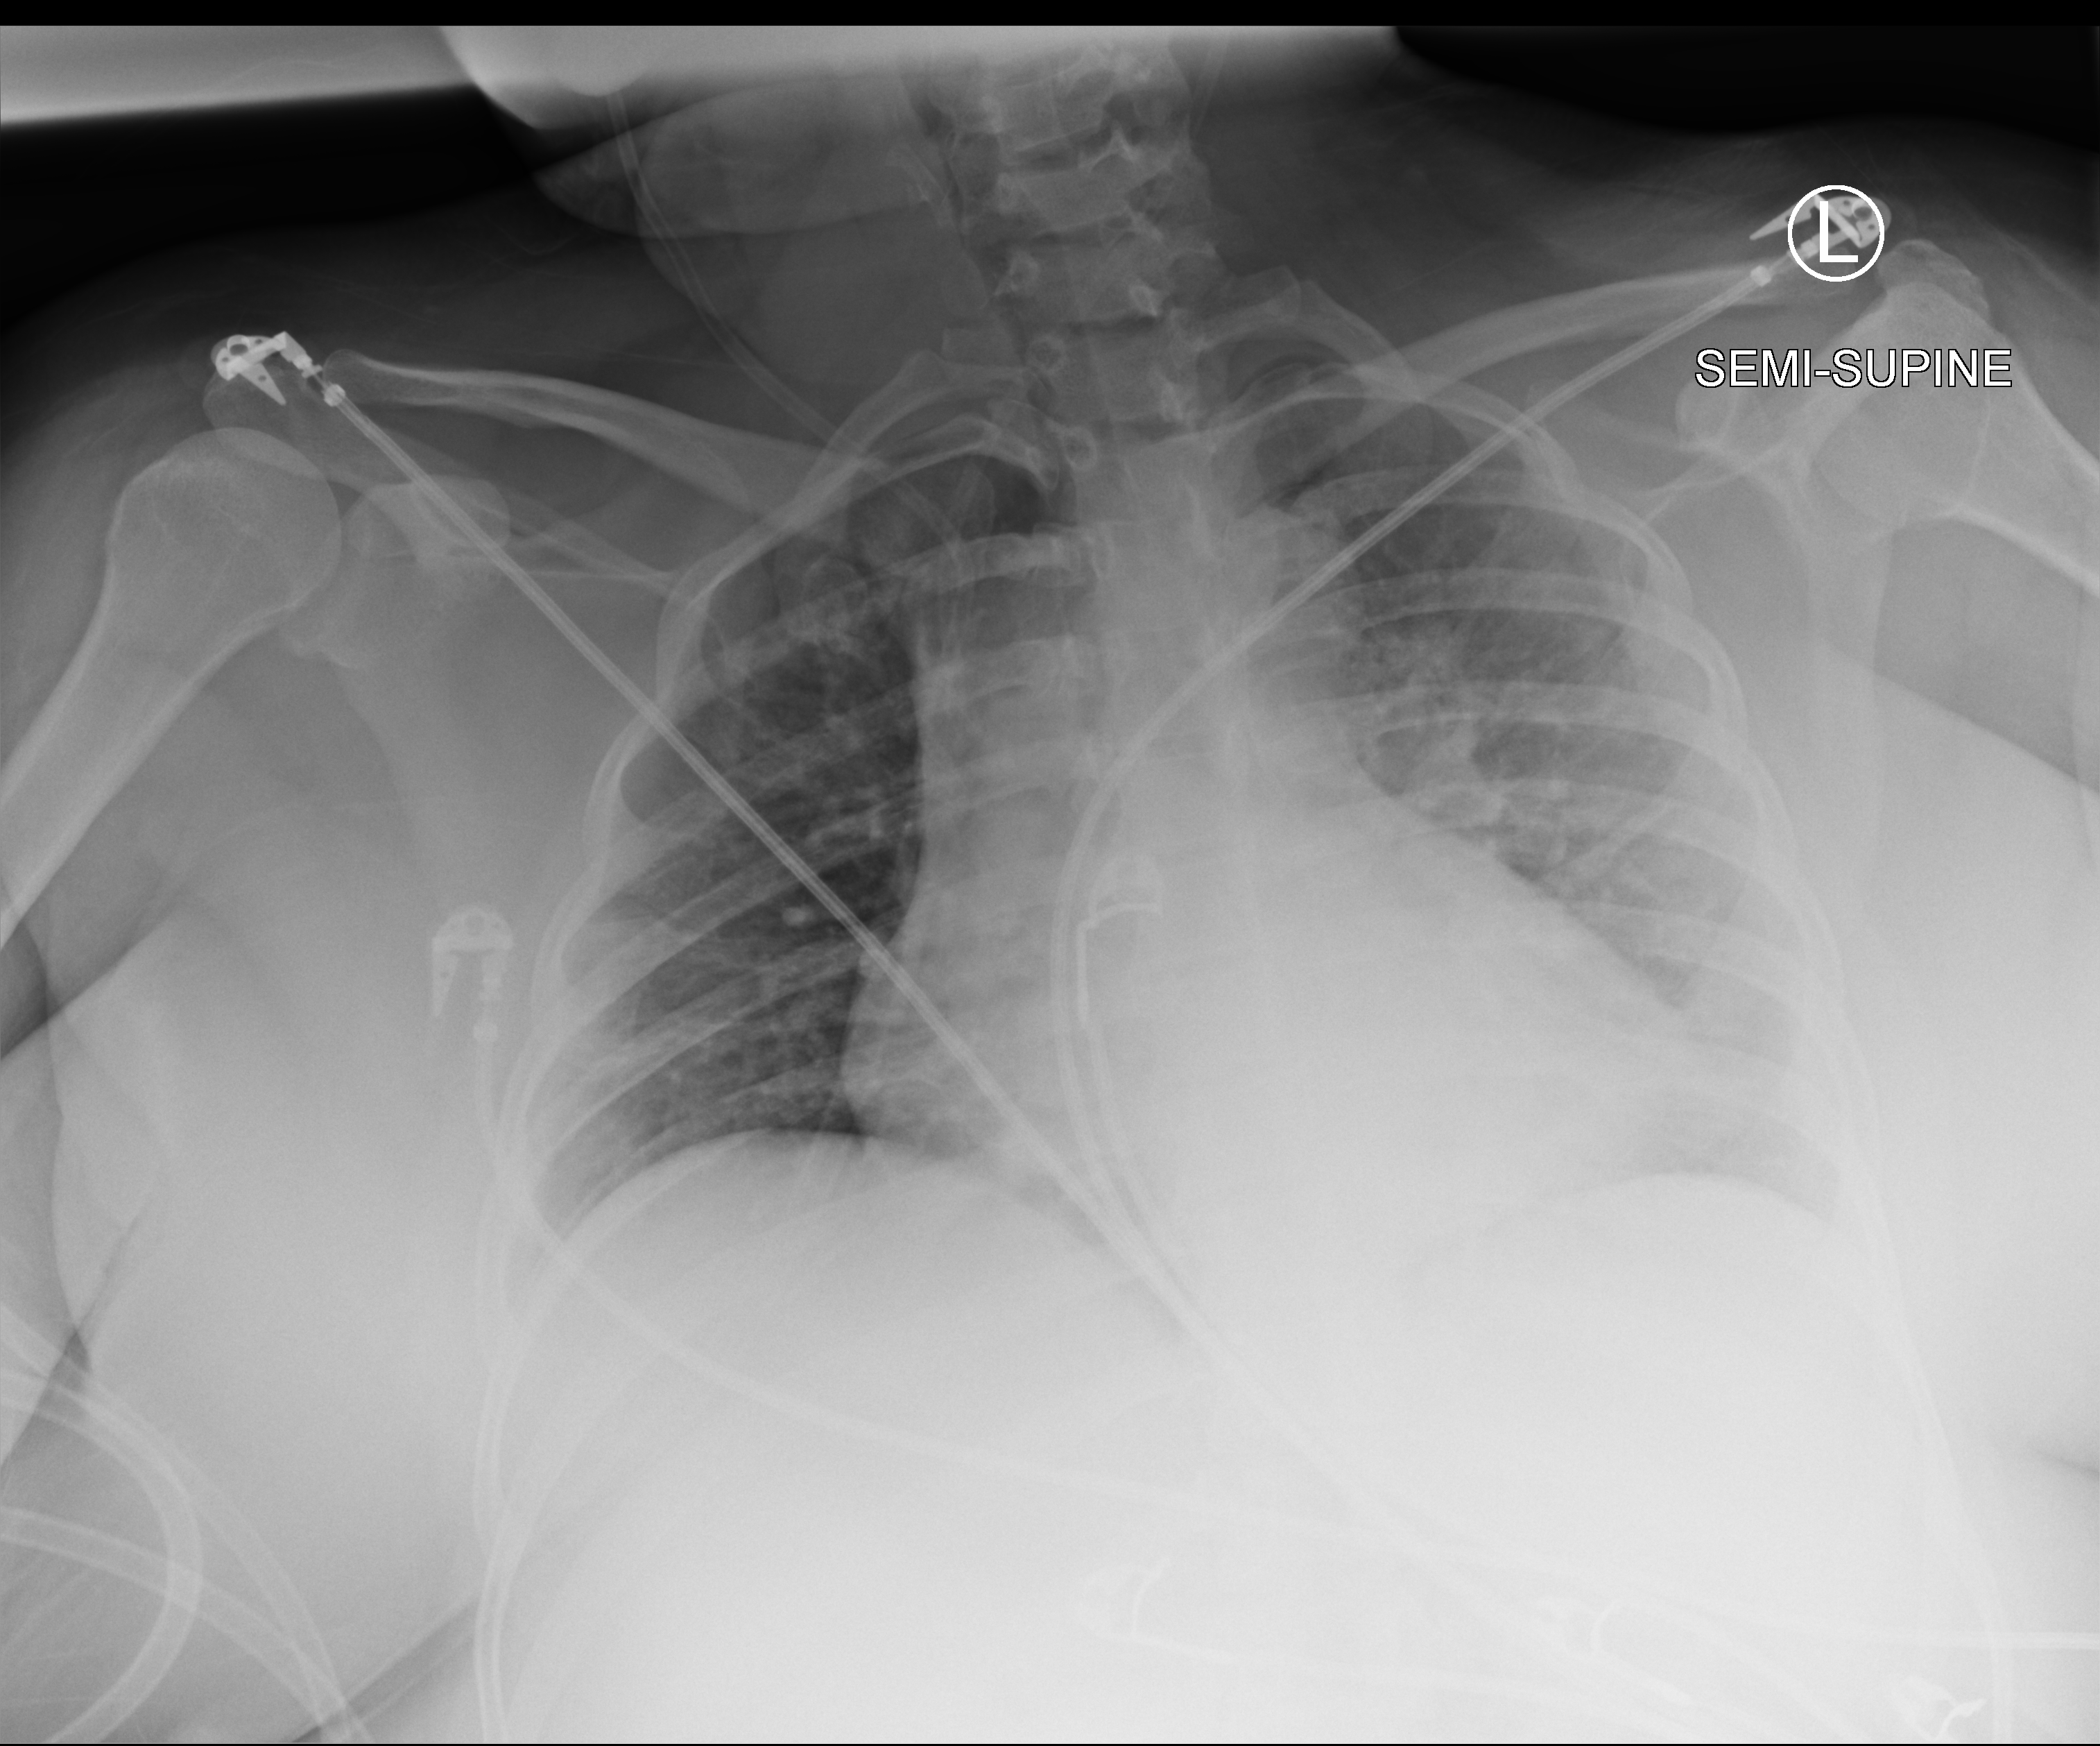
Bedside chest radiograph (computed radiography), anteroposterior (AP) projection. Female patient hospitalised with COVID-19, age 18–59 years.
Hospital-stay facts (about this admission, not read from this image; timing relative to this image not recorded):
- admitted to intensive care during this hospital stay: no
- mechanically ventilated during this hospital stay: no